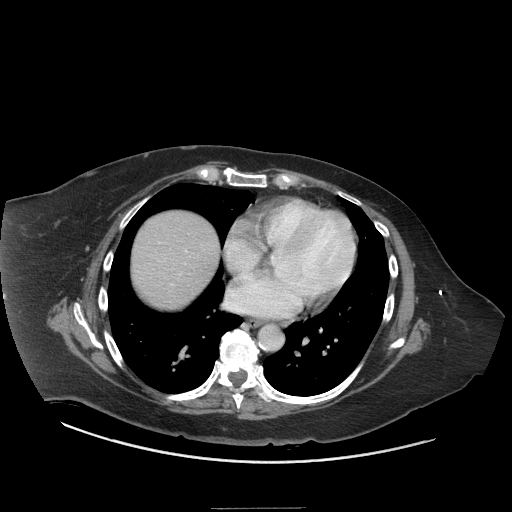
Contrast-enhanced abdominal CT (liver protocol), one axial slice; position 72 of 81 along the scan axis; reconstruction kernel STANDARD; 140 kVp; soft-tissue window (W 400 / L 40 HU); 2.5 mm slice thickness; 512 × 512 image matrix, field of view 440 × 440 mm. From the clinical record (not read from this slice): diagnosis: hepatocellular carcinoma (patient treated with transarterial chemoembolisation; whether this scan precedes or follows treatment is not stated here); TNM stage (as recorded): Stage-II; Child-Pugh class: A; tumour nodularity: multinodular; tumour size: 1.7 cm.
Outlined on this slice (semi-automatic segmentation, software-assisted and operator-edited):
- liver parenchyma outside the tumour (the mass and vessels are separate outlines, so this box may not span the whole liver): bounding box (x1, y1, x2, y2) in pixels: (132, 210, 218, 308)
- liver vessels: (158, 242, 187, 286)